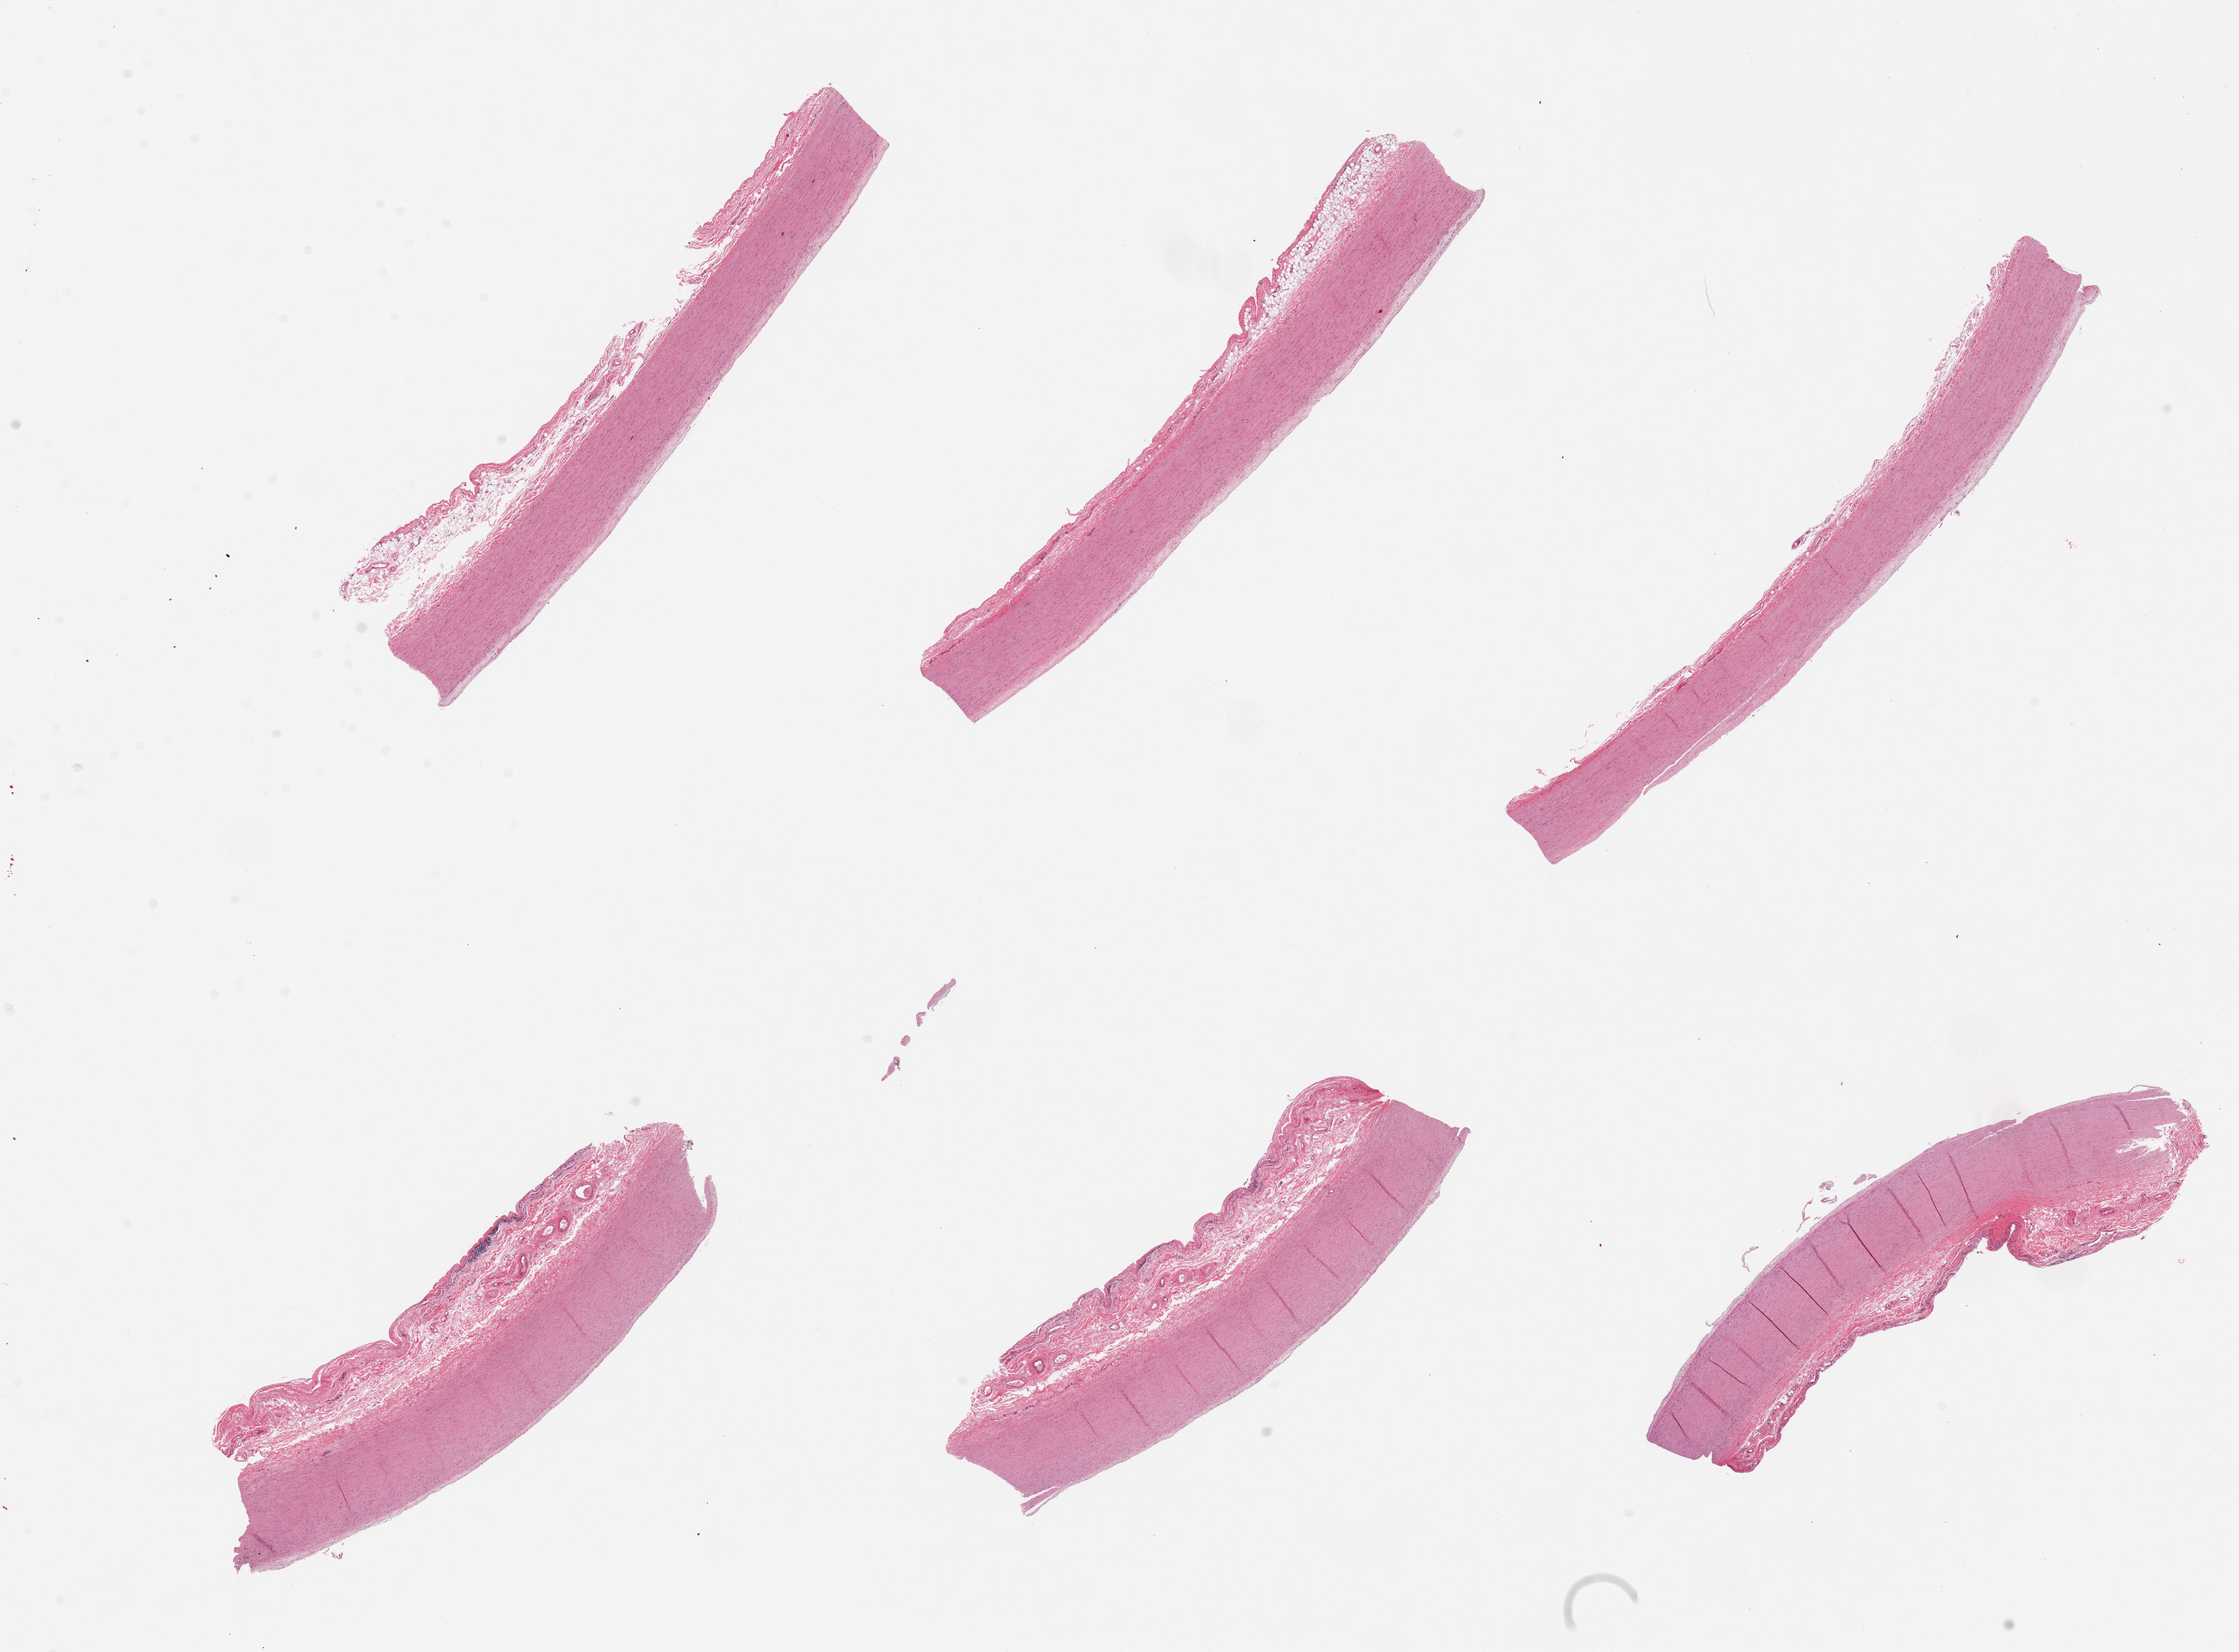
H&E whole-slide image — whole scanned area (about 25.6 x 18.9 mm, slide scanned at 20x) shown as a low-resolution overview. PAXgene-fixed, paraffin-embedded tissue. Sampled site (target tissue): aorta. Donor tissue sample. Donor: female.
Reviewer comment on this tissue sample: 6 pieces, adherent serosa up to ~1mm on several sections.